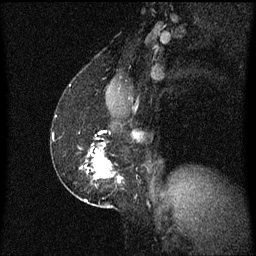
Breast MRI (dynamic contrast-enhanced), one sagittal slice; slice 37 of 60 in the series (ordered by position); dynamic contrast-enhanced series, image 2 of 3 at this slice position (ordered by acquisition); 1.5 T; TE 4.2 ms, TR 8.4 ms; 2 mm slice thickness; 256 × 256 image matrix. Patient: female, 52 years. Case-level facts recorded for this patient, not image findings: setting: breast cancer imaged before/during neoadjuvant chemotherapy; receptor status: HER2-positive.
Structures marked on this image (semi-automatic segmentation, software-assisted and operator-edited):
- analysis volume of interest (the breast-tissue region the enhancement analysis was run in; not a lesion): box from (x=63, y=142) to (x=122, y=203) px
- tumour enhancement mask (voxels above the 70 % enhancement threshold inside the analysis volume of interest): (x=88, y=142)–(x=122, y=183)